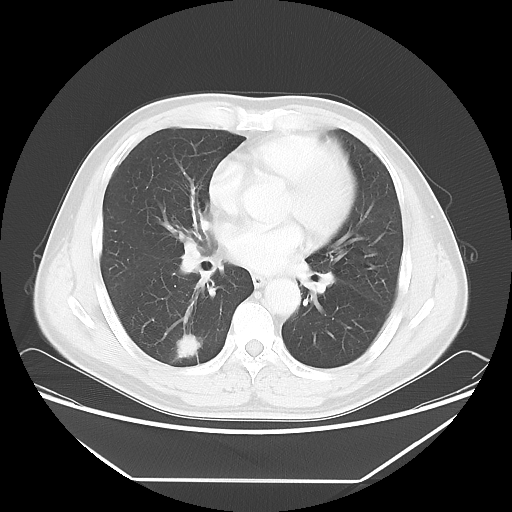
Chest CT, one axial slice; position 32 of 65 along the scan axis; reconstruction kernel LUNG; 120 kVp; lung window (W 1500 / L -600 HU); 5 mm slice thickness; 512 × 512 image matrix, field of view 418 × 418 mm. Male patient, age 50 years. From the clinical record (not read from this slice): clinical TNM (as recorded): T1c N0 M0; histopathological grade: G3.
Annotated regions visible in this slice (bounding box drawn by a radiologist):
- lung tumour (recorded histology: adenocarcinoma): bounding box <172,331,205,363> (left, top, right, bottom; pixels)